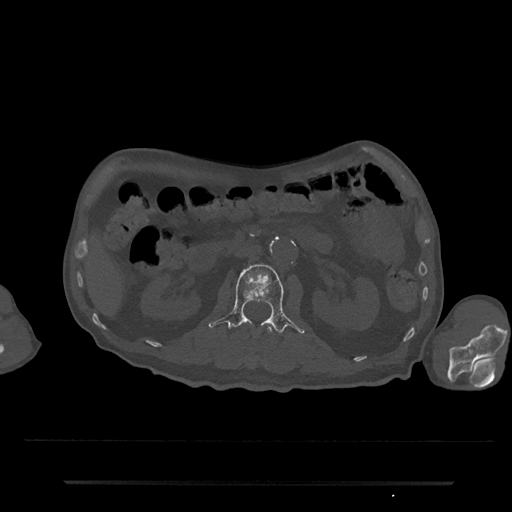
CT including the spine, one axial slice; position 75 of 797 along the scan axis; reconstruction kernel Br40s/3; bone window (W 1800 / L 400 HU); 0.5 mm slice thickness; 512 × 512 image matrix, field of view 427 × 427 mm. Male patient, age 74 years. From the clinical record (not read from this slice): primary cancer: prostate.
Outlined on this slice (semi-automatically segmented with operator editing):
- L1 vertebra: bounding box <249,325,273,364> (left, top, right, bottom; pixels)
- L2 vertebra: <209,264,305,335>